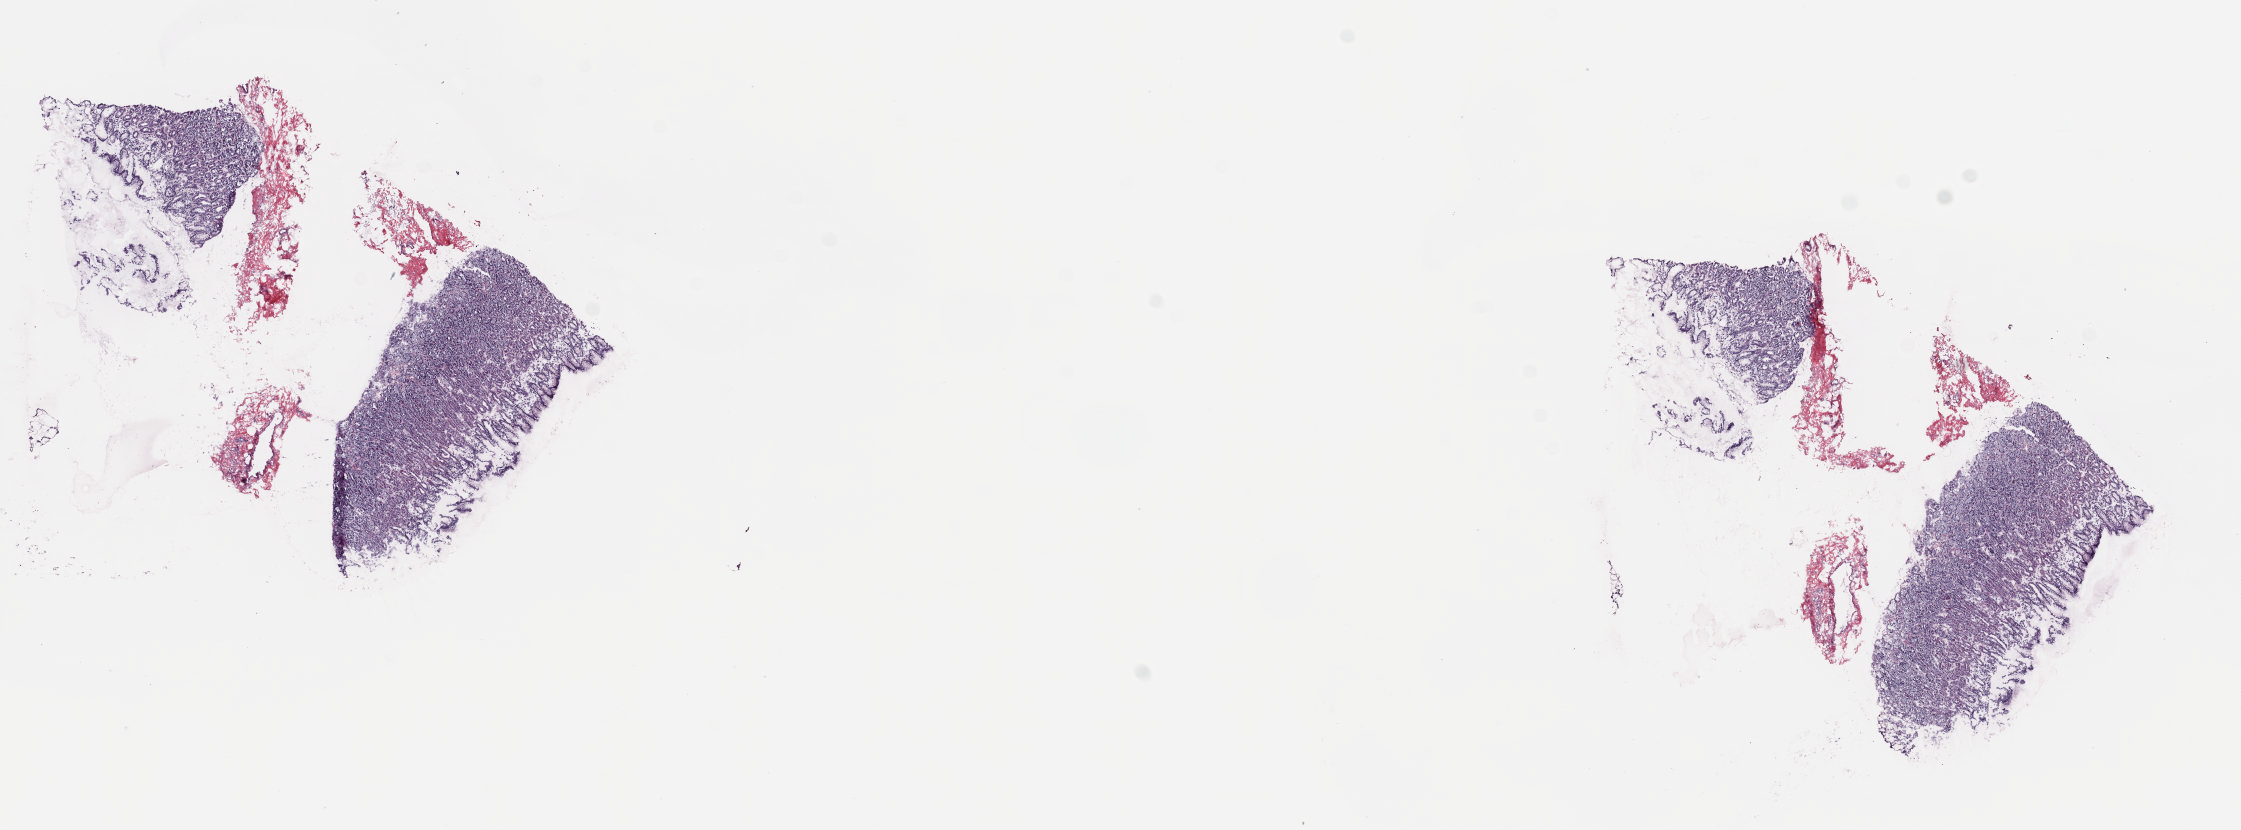
H&E whole-slide image — low-resolution overview of the scanned area, about 17.7 x 6.6 mm, frozen section from the top of the tissue portion, sample: solid tissue normal (non-tumour tissue), esophagus. Male patient; age at initial diagnosis 81 years. Slide review estimates, as recorded: tumour cells 0%, tumour nuclei 0%, normal cells 70%, stromal cells 30%, necrosis 0%. Infiltration values recorded for this section: lymphocyte infiltration 2%, monocyte infiltration 0%, neutrophil infiltration 0%.
This section: solid tissue normal sample (biorepository sample class). Patient diagnosis: Mucinous adenocarcinoma.